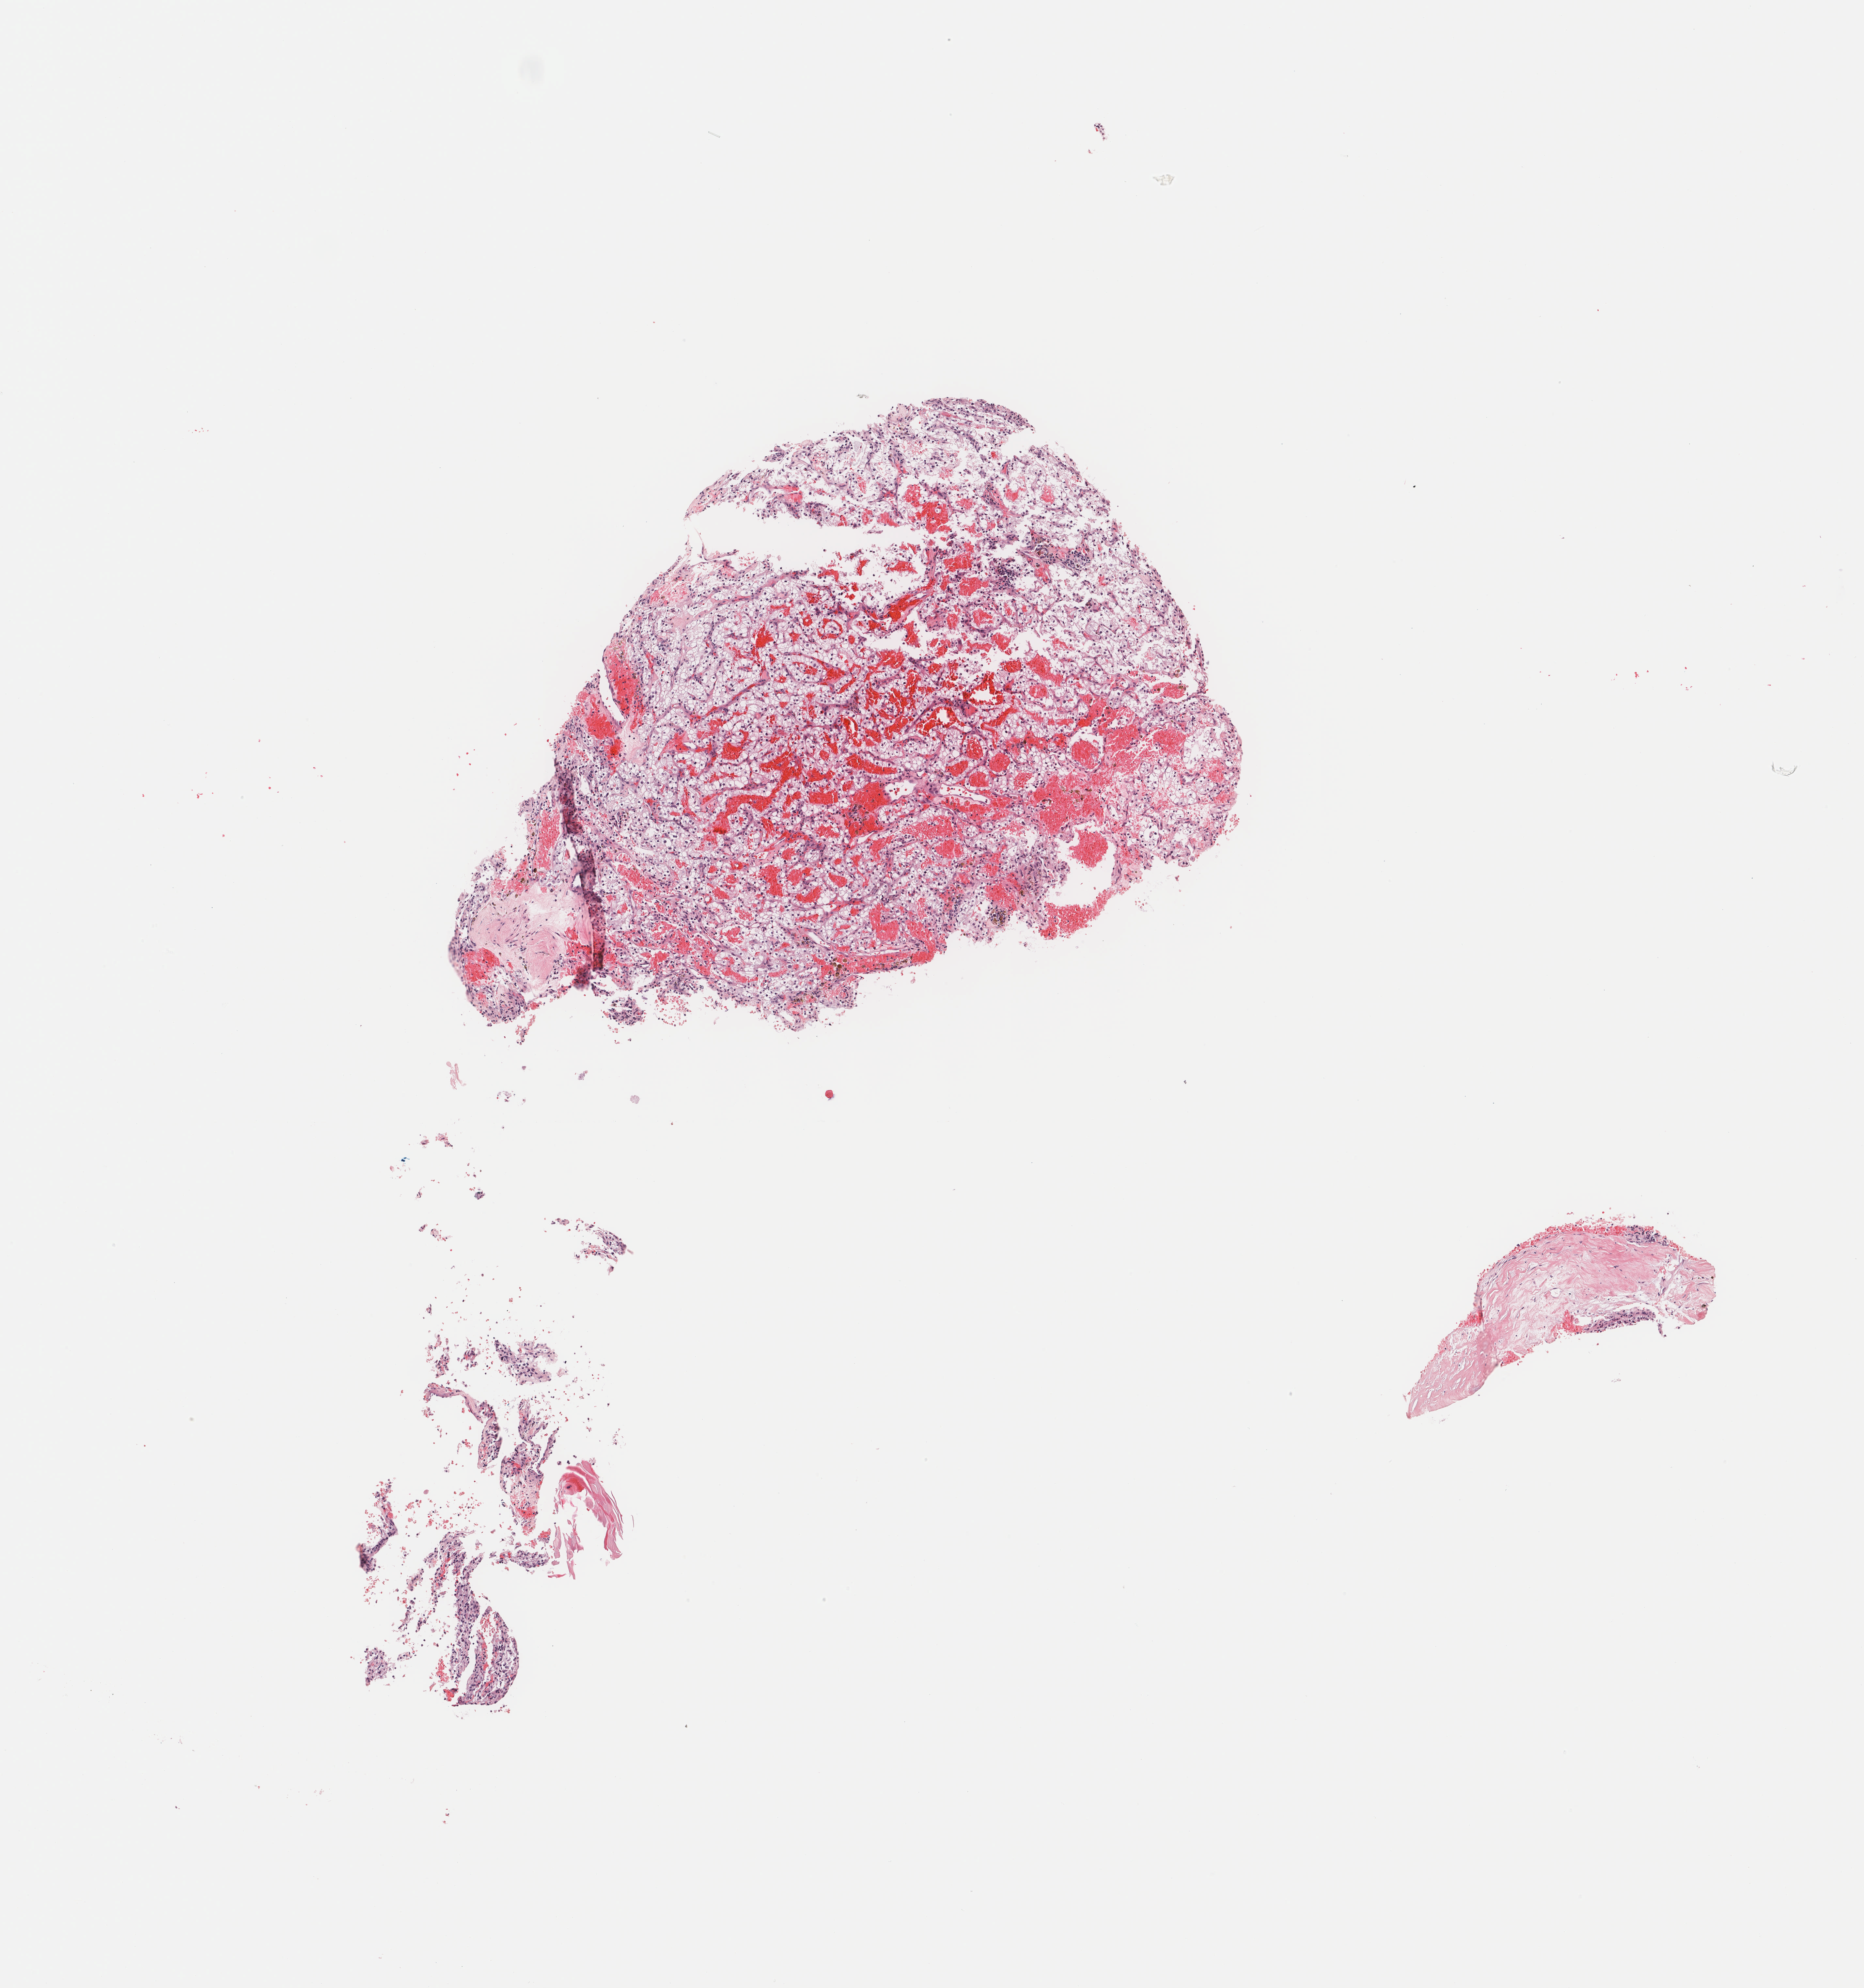
H&E-stained whole-slide image — shown as a low-resolution overview of the whole scanned area (about 5.7 x 6.0 mm, acquisition: 40x scan); frozen section from the bottom of the tissue portion; primary tumour sample from the kidney. Male patient; age at initial diagnosis 56 years. Histologic grade: G2 (moderately differentiated). Composition of this section per pathologist review: tumour cells 90%, tumour nuclei 92%, normal cells 0%, stromal cells 10%, necrosis 0%. Inflammatory infiltration, as recorded: lymphocyte infiltration 3%, monocyte infiltration 1%, neutrophil infiltration 0%.
TNM: T1b N0 M0. Diagnosis: Clear cell adenocarcinoma, NOS. AJCC pathologic stage: I.